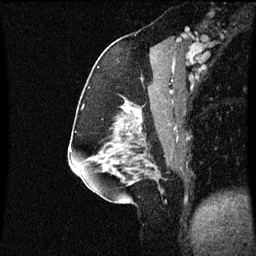
Breast MRI (dynamic contrast-enhanced), one sagittal slice; position 28 of 60 along the scan axis; dynamic contrast-enhanced series, image 2 of 3 at this slice position (ordered by acquisition); 1.5 T; TE 4.2 ms, TR 8.9 ms; 2 mm slice thickness; 256 × 256 image matrix, field of view 200 × 200 mm. Patient: female, 58 years. From the clinical record (not read from this slice): setting: breast cancer imaged before/during neoadjuvant chemotherapy; receptor status: triple-negative.
Annotated regions visible in this slice (semi-automatically segmented with operator editing):
- analysis volume of interest (the breast-tissue region the enhancement analysis was run in; not a lesion): box from (x=104, y=118) to (x=171, y=179) px
- tumour enhancement mask (voxels above the 70 % enhancement threshold inside the analysis volume of interest): (x=118, y=118)–(x=143, y=175)